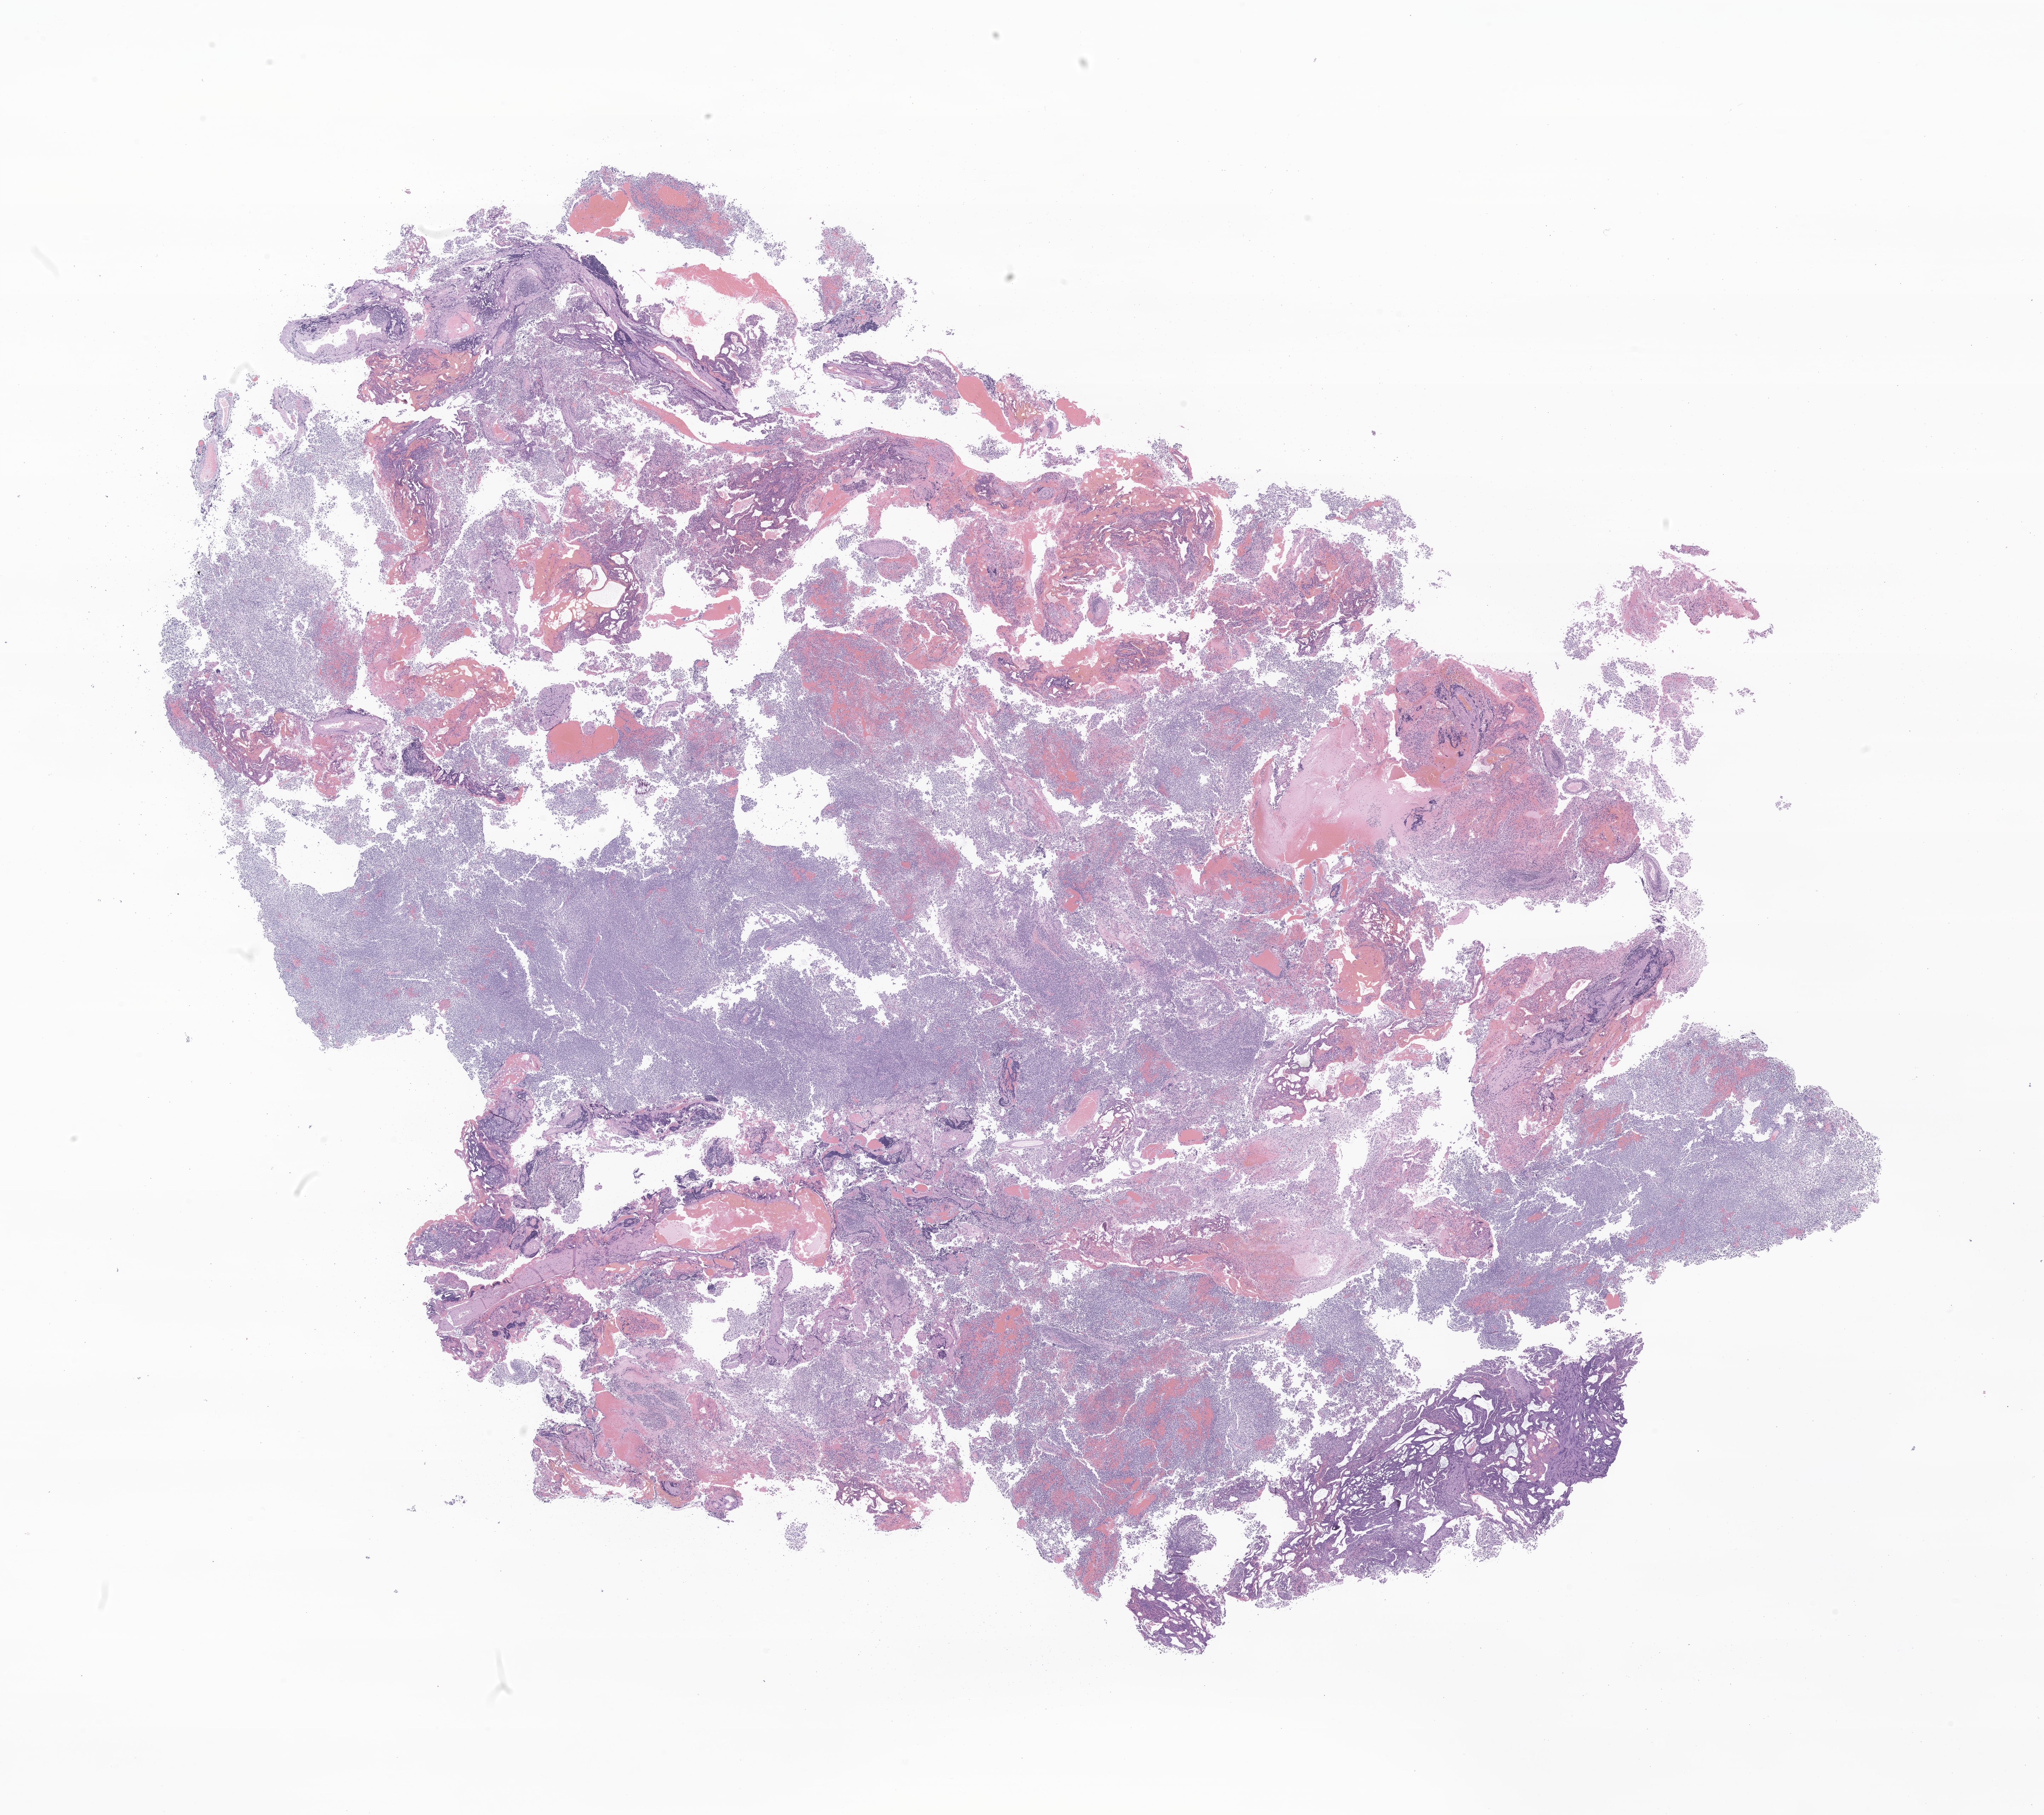
Whole-slide image, hematoxylin and eosin (H&E) stain of tumor tissue from the cerebral ventricle, low-resolution overview of the scanned area, about 24.4 x 21.6 mm. Formalin-fixed paraffin-embedded section. Patient male; age 135 months (11 years 3 months).
Diagnosis: Medulloblastoma, non-WNT/non-SHH.